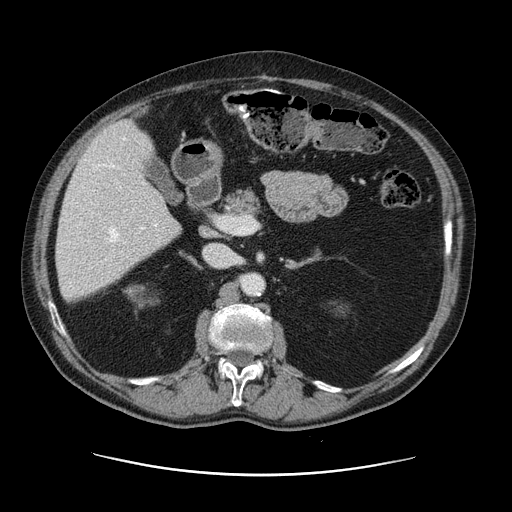
Contrast-enhanced abdominal CT, one axial slice; slice 64 of 141 in the series (ordered by position); intravenous contrast given; soft-tissue window (W 400 / L 40 HU); 2.5 mm slice thickness; 512 × 512 image matrix, field of view 395 × 395 mm. Male patient, age 72 years. From the clinical record (not read from this slice): diagnosis: colorectal cancer liver metastases, imaged before liver resection; multiple liver metastases: yes; largest metastasis: 5.4 cm; disease in both lobes: yes.
Structures marked on this image (expert manual segmentation):
- hepatic veins: box from (x=96, y=138) to (x=145, y=242) px
- liver: (x=57, y=122)–(x=180, y=301)
- planned liver remnant (the part of the liver to remain after resection): (x=57, y=186)–(x=181, y=301)
- portal vein (with intrahepatic branches): (x=135, y=226)–(x=146, y=239)